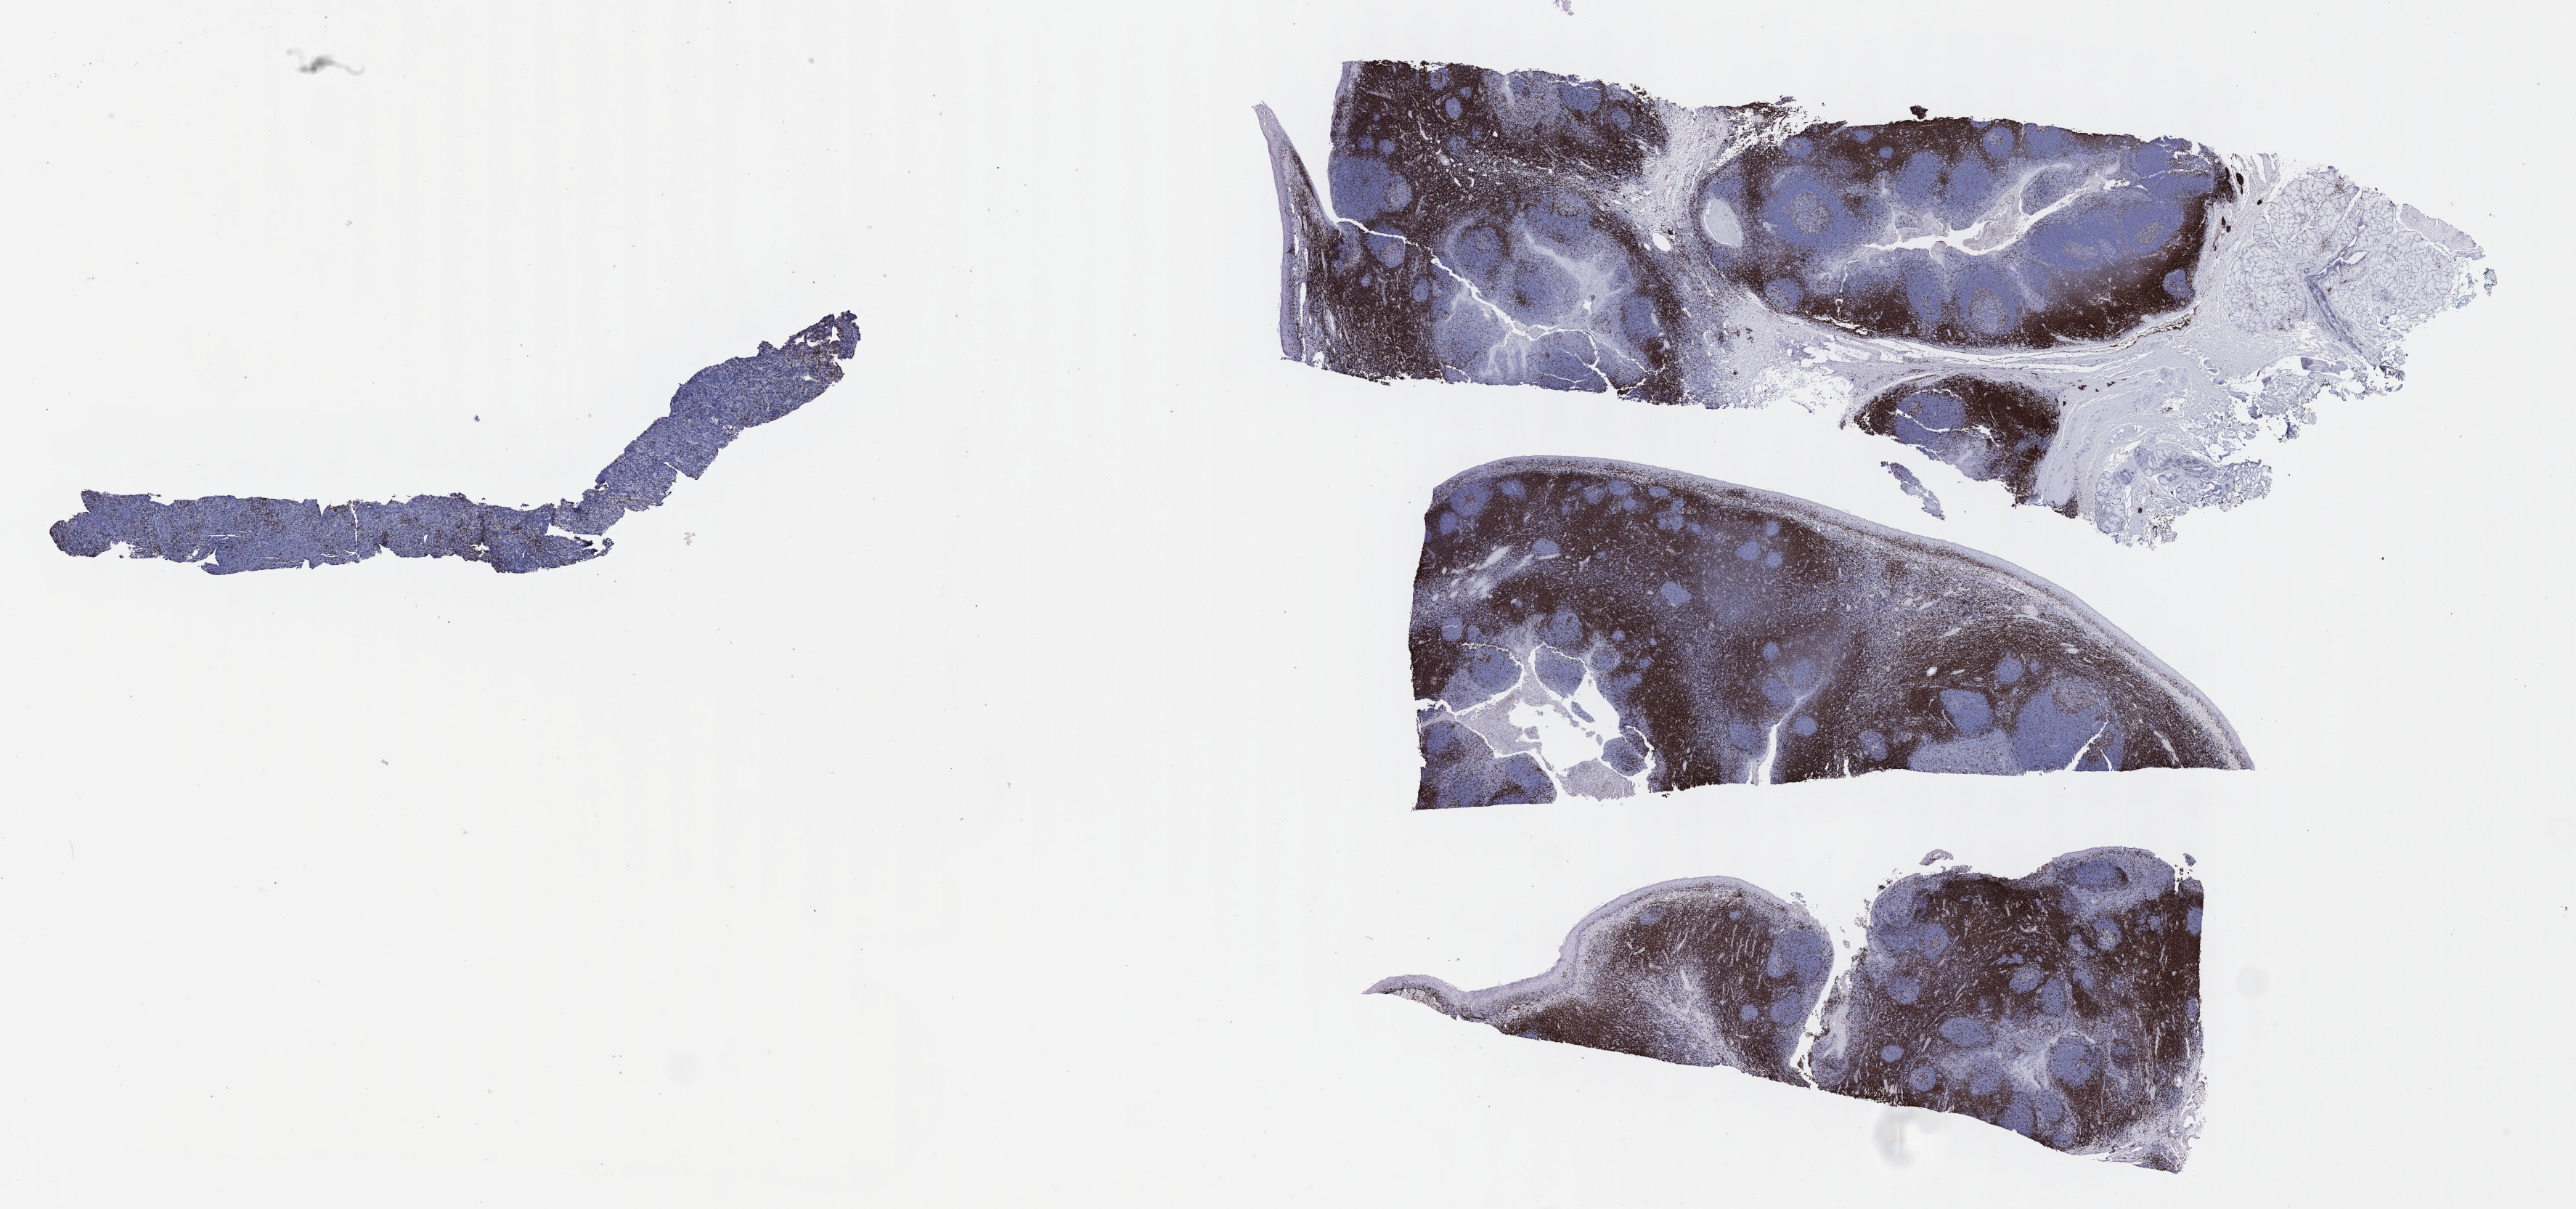
Immunohistochemistry (IHC) whole-slide image stained for CD3, a low-resolution overview of the entire scanned area, about 28.7 x 13.5 mm; specimen: tumor tissue; anatomic site: kidney. Male, age 9 years at initial diagnosis.
Histologic diagnosis: Burkitt lymphoma, NOS.